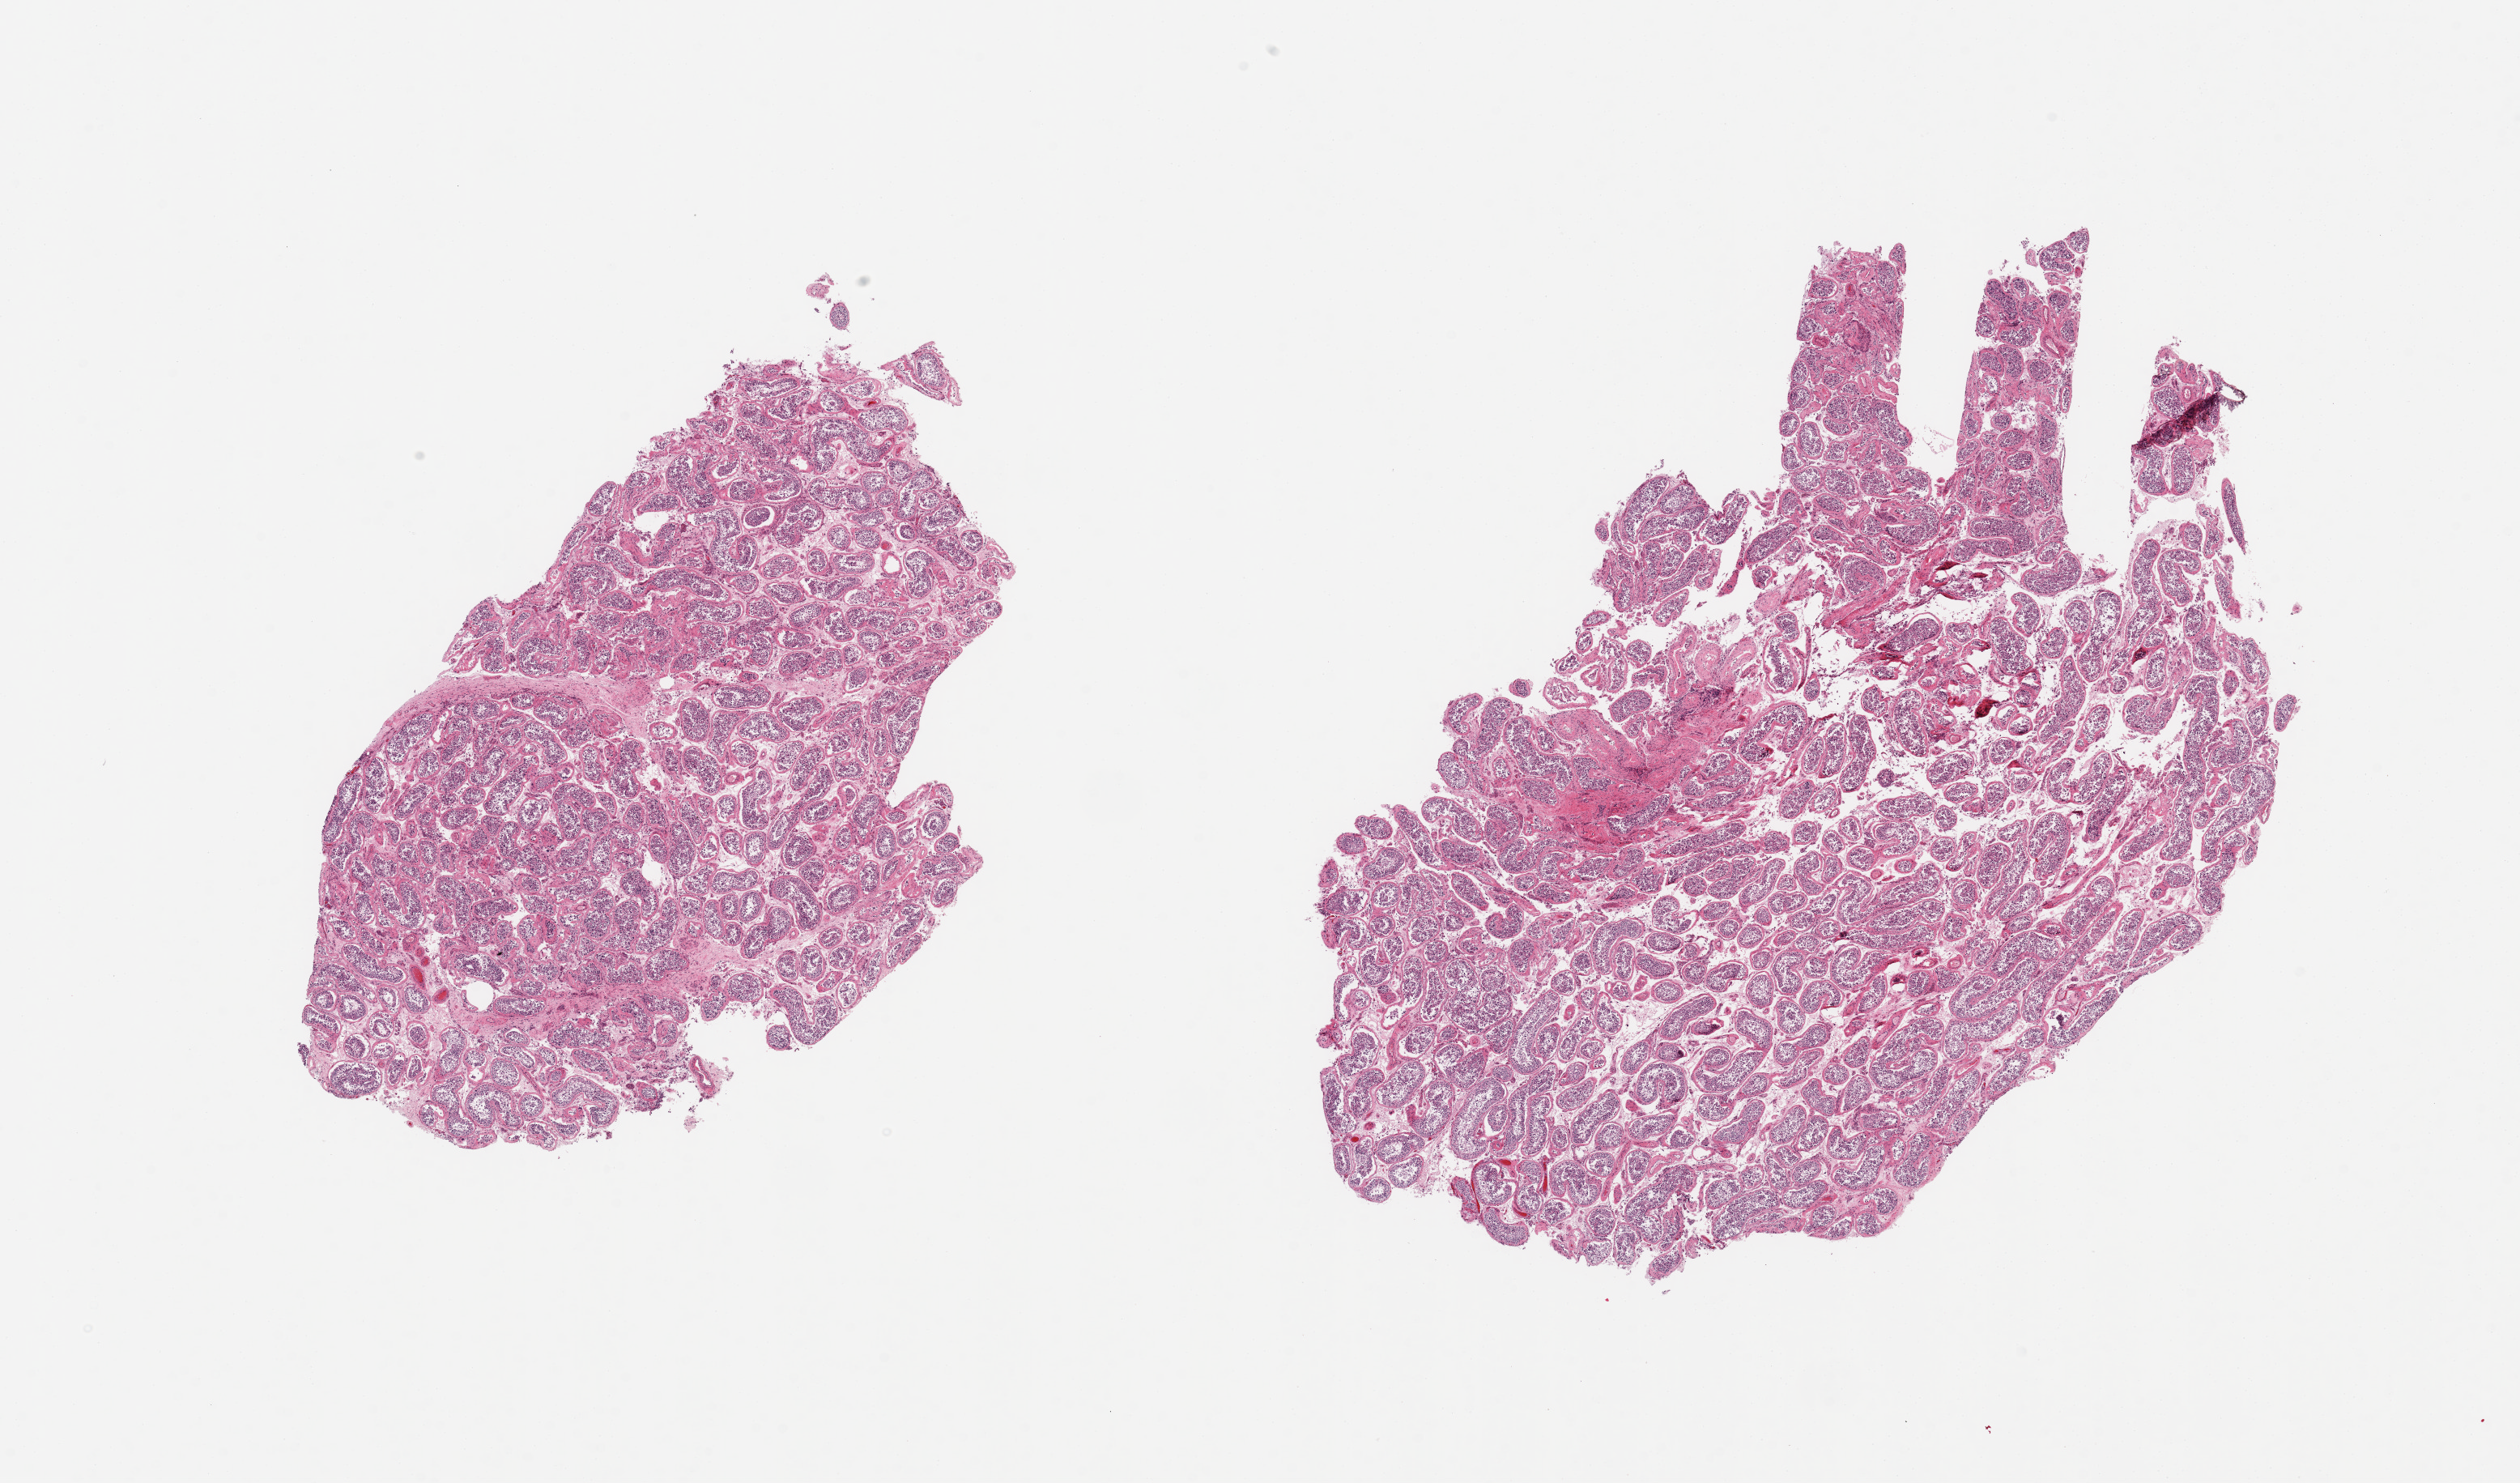
Digitized H&E-stained section, brightfield, shown as a low-resolution overview of the whole scanned area (about 24.6 x 14.5 mm, from a 20x scan); PAXgene-fixed, paraffin-embedded tissue; section of testis (target tissue); tissue donor sample. Donor: male.
Review note (as recorded): 2 pieces, spermatogenesis is present but appears reduced.